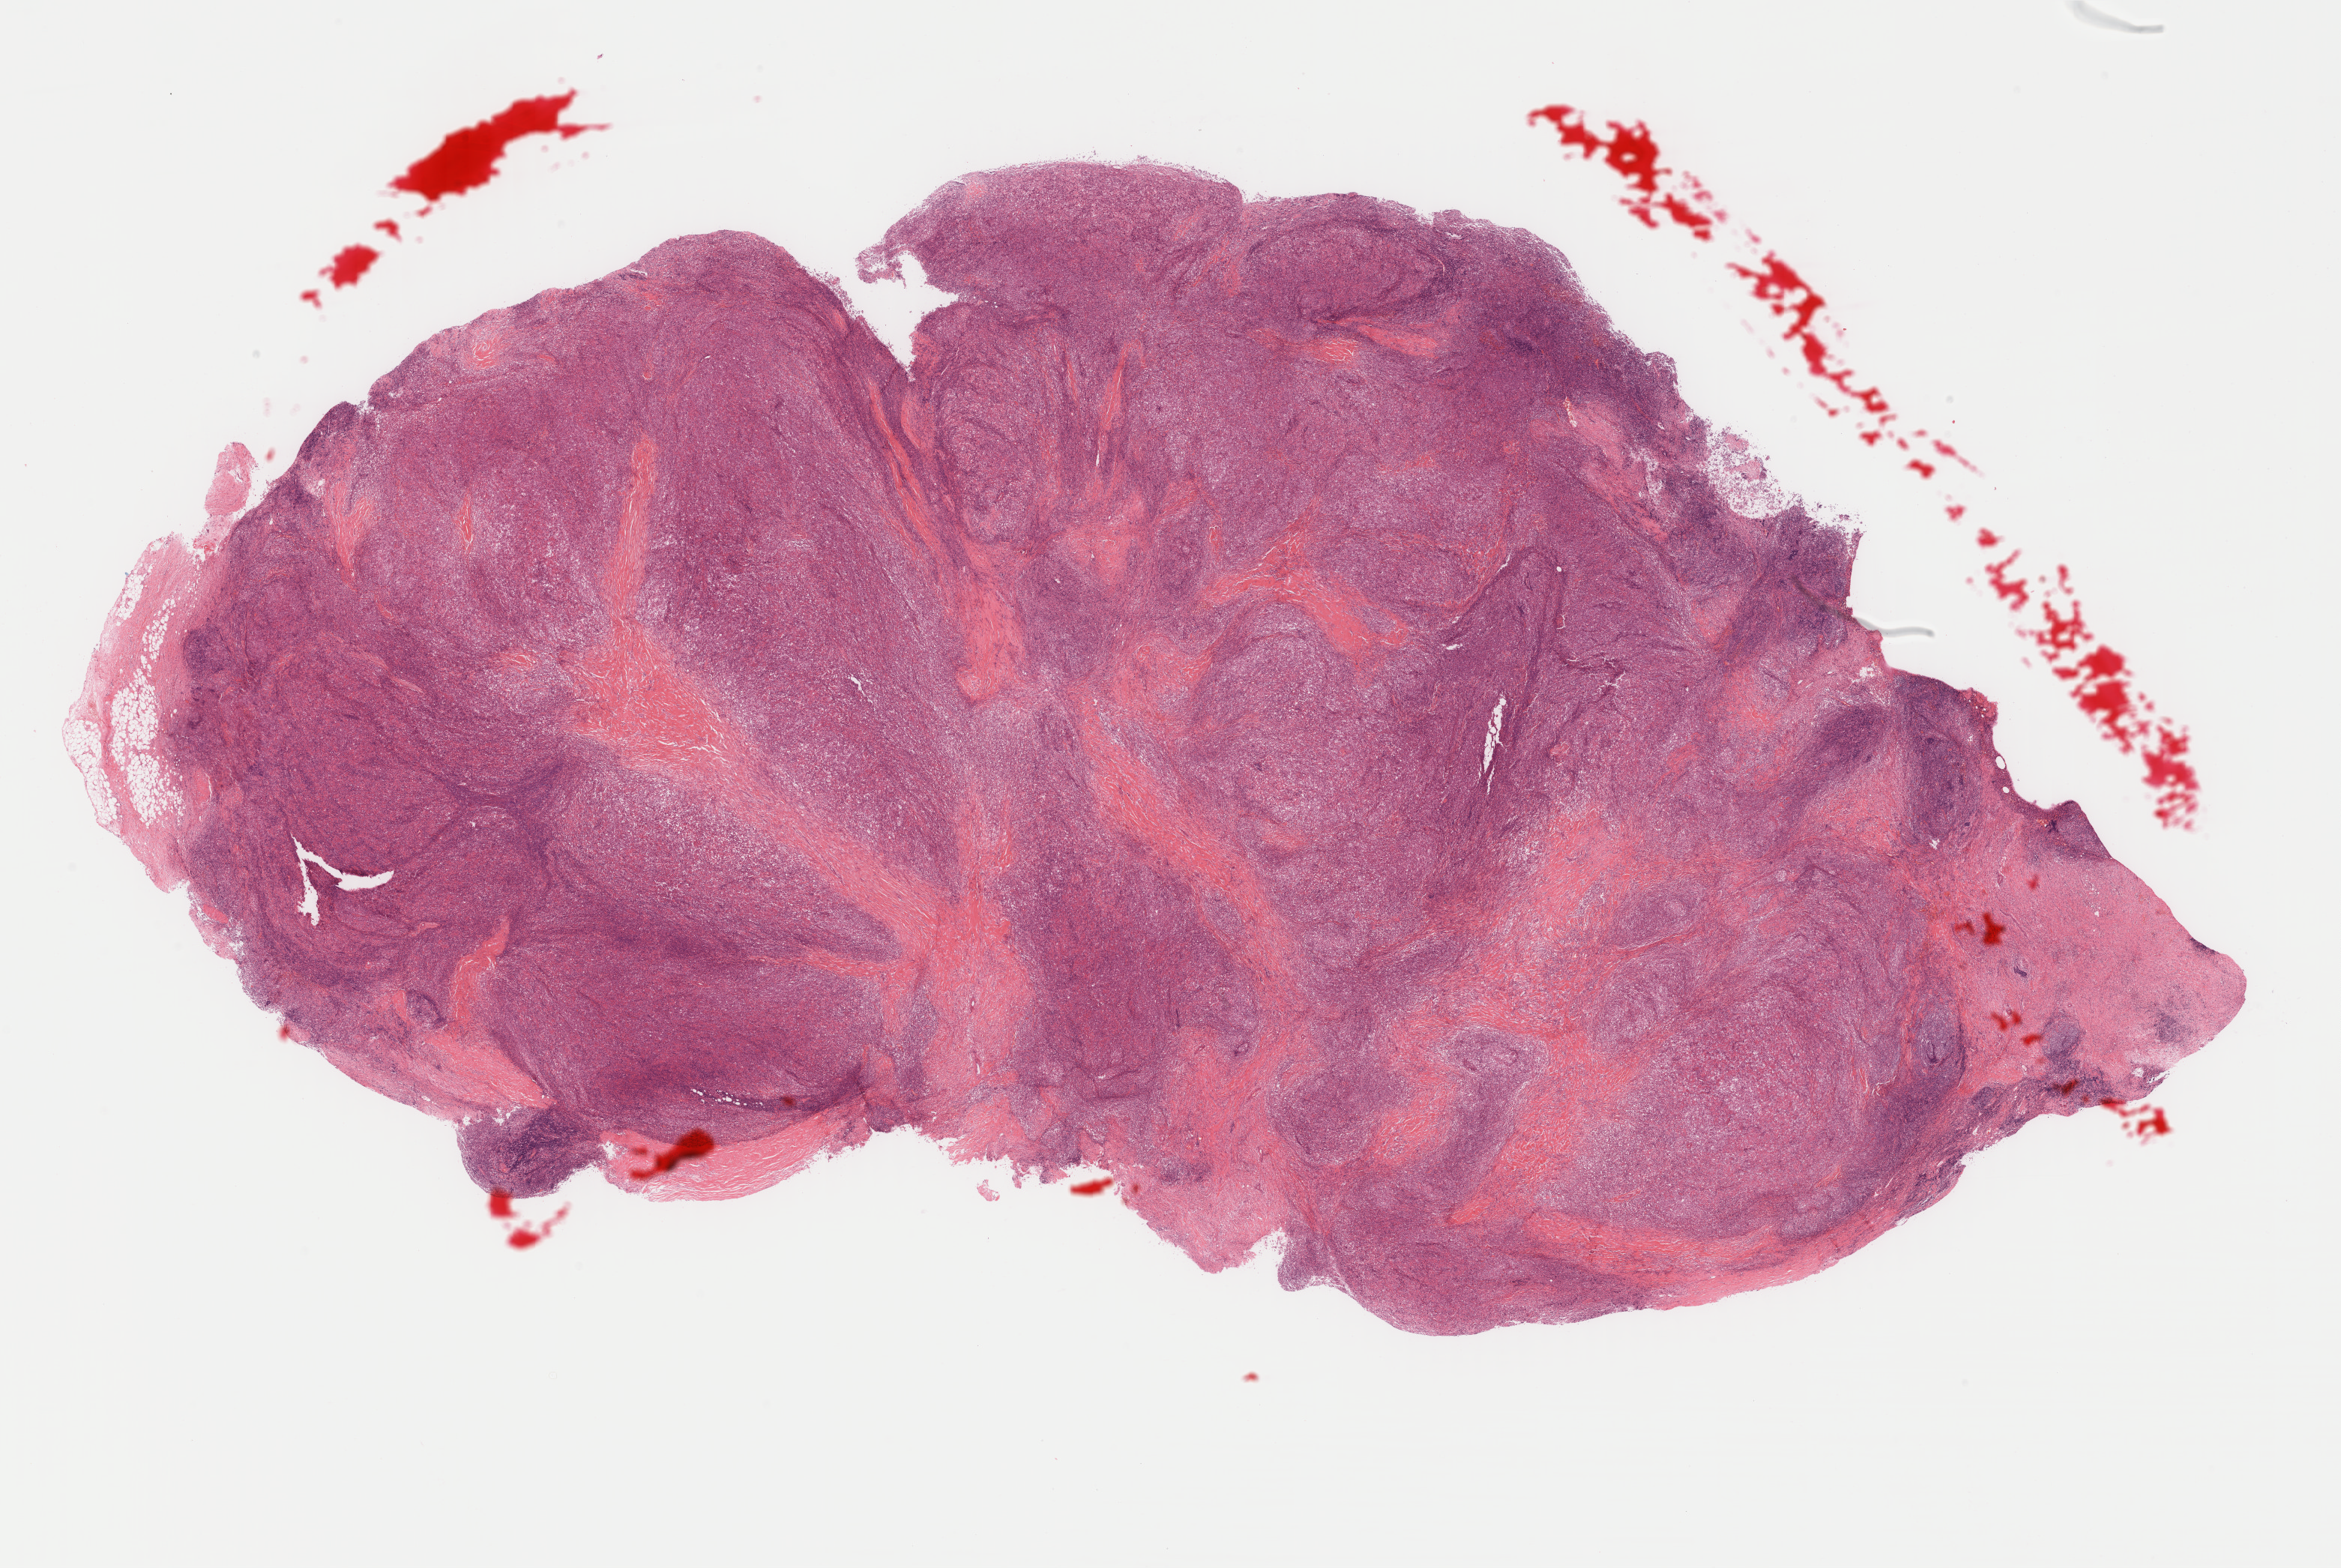
Whole-slide histology image, H&E, a low-resolution overview of the entire scanned area, about 24.8 x 16.6 mm (acquisition: 40x scan), formalin-fixed paraffin-embedded (FFPE) diagnostic section, lymphoid tissue, primary tumour sample. Patient: male, age at initial diagnosis 67 years.
Diagnosis: Diffuse large B-cell lymphoma, NOS (lymph nodes of axilla or arm).